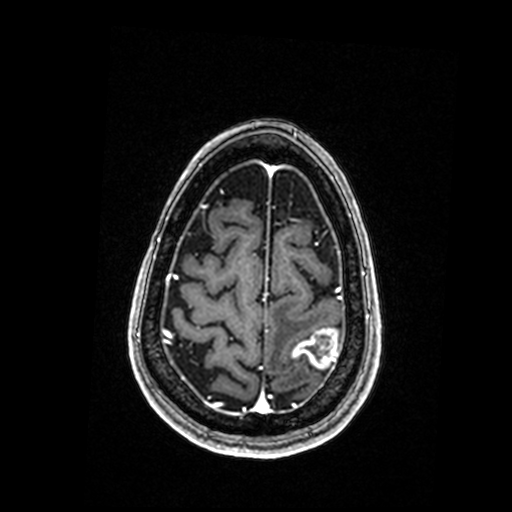
Brain MRI from a brain-tumour surgery series, one axial slice. Position 44 of 192 along the scan axis. T1-weighted post-contrast. 512 × 512 image matrix, field of view 250 × 250 mm. From the clinical record (not read from this slice): histopathology: Metastastic Carcinoma, Poorly Differentiated; tumour location: Left Parietal.
Annotated regions visible in this slice (outlined manually by an expert reader):
- tumour: bounding box (x1, y1, x2, y2) in pixels: (293, 330, 338, 369)